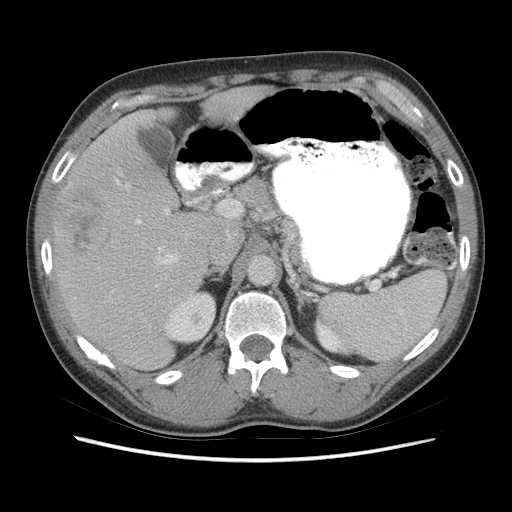
Contrast-enhanced abdominal CT (liver protocol), one axial slice; slice 39 of 73 in the series (ordered by position); soft-tissue window (W 400 / L 40 HU); 2.5 mm slice thickness; 512 × 512 image matrix, field of view 360 × 360 mm. From the clinical record (not read from this slice): diagnosis: hepatocellular carcinoma (patient treated with transarterial chemoembolisation; whether this scan precedes or follows treatment is not stated here); TNM stage (as recorded): Stage-IIIA; Child-Pugh class: A.
Structures marked on this image (semi-automatic segmentation, software-assisted and operator-edited):
- liver parenchyma outside the tumour (the mass and vessels are separate outlines, so this box may not span the whole liver): bounding box (x1, y1, x2, y2) in pixels: (52, 86, 270, 370)
- mass: (59, 188, 112, 258)
- liver vessels: (116, 180, 177, 287)